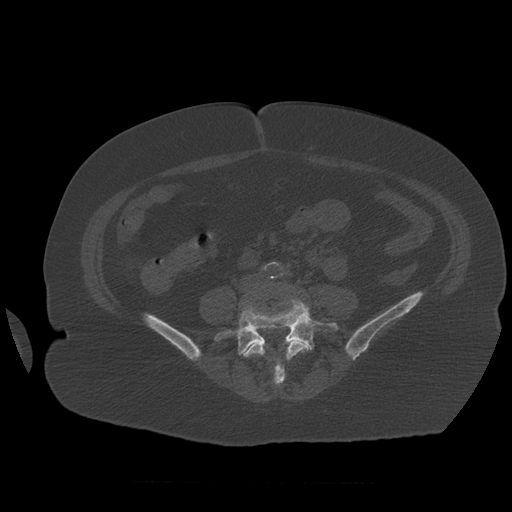
CT including the spine, one axial slice; reconstruction kernel STANDARD; bone window (W 1800 / L 400 HU); 1.25 mm slice thickness; 512 × 512 image matrix, field of view 404 × 404 mm. Patient age 81 years. From the clinical record (not read from this slice): primary cancer: renal; vertebrae with lytic lesions (as recorded): L1.
Outlined on this slice (semi-automatic segmentation, software-assisted and operator-edited):
- L4 vertebra: bounding box (x1, y1, x2, y2) in pixels: (244, 337, 310, 386)
- L5 vertebra: (215, 299, 339, 356)